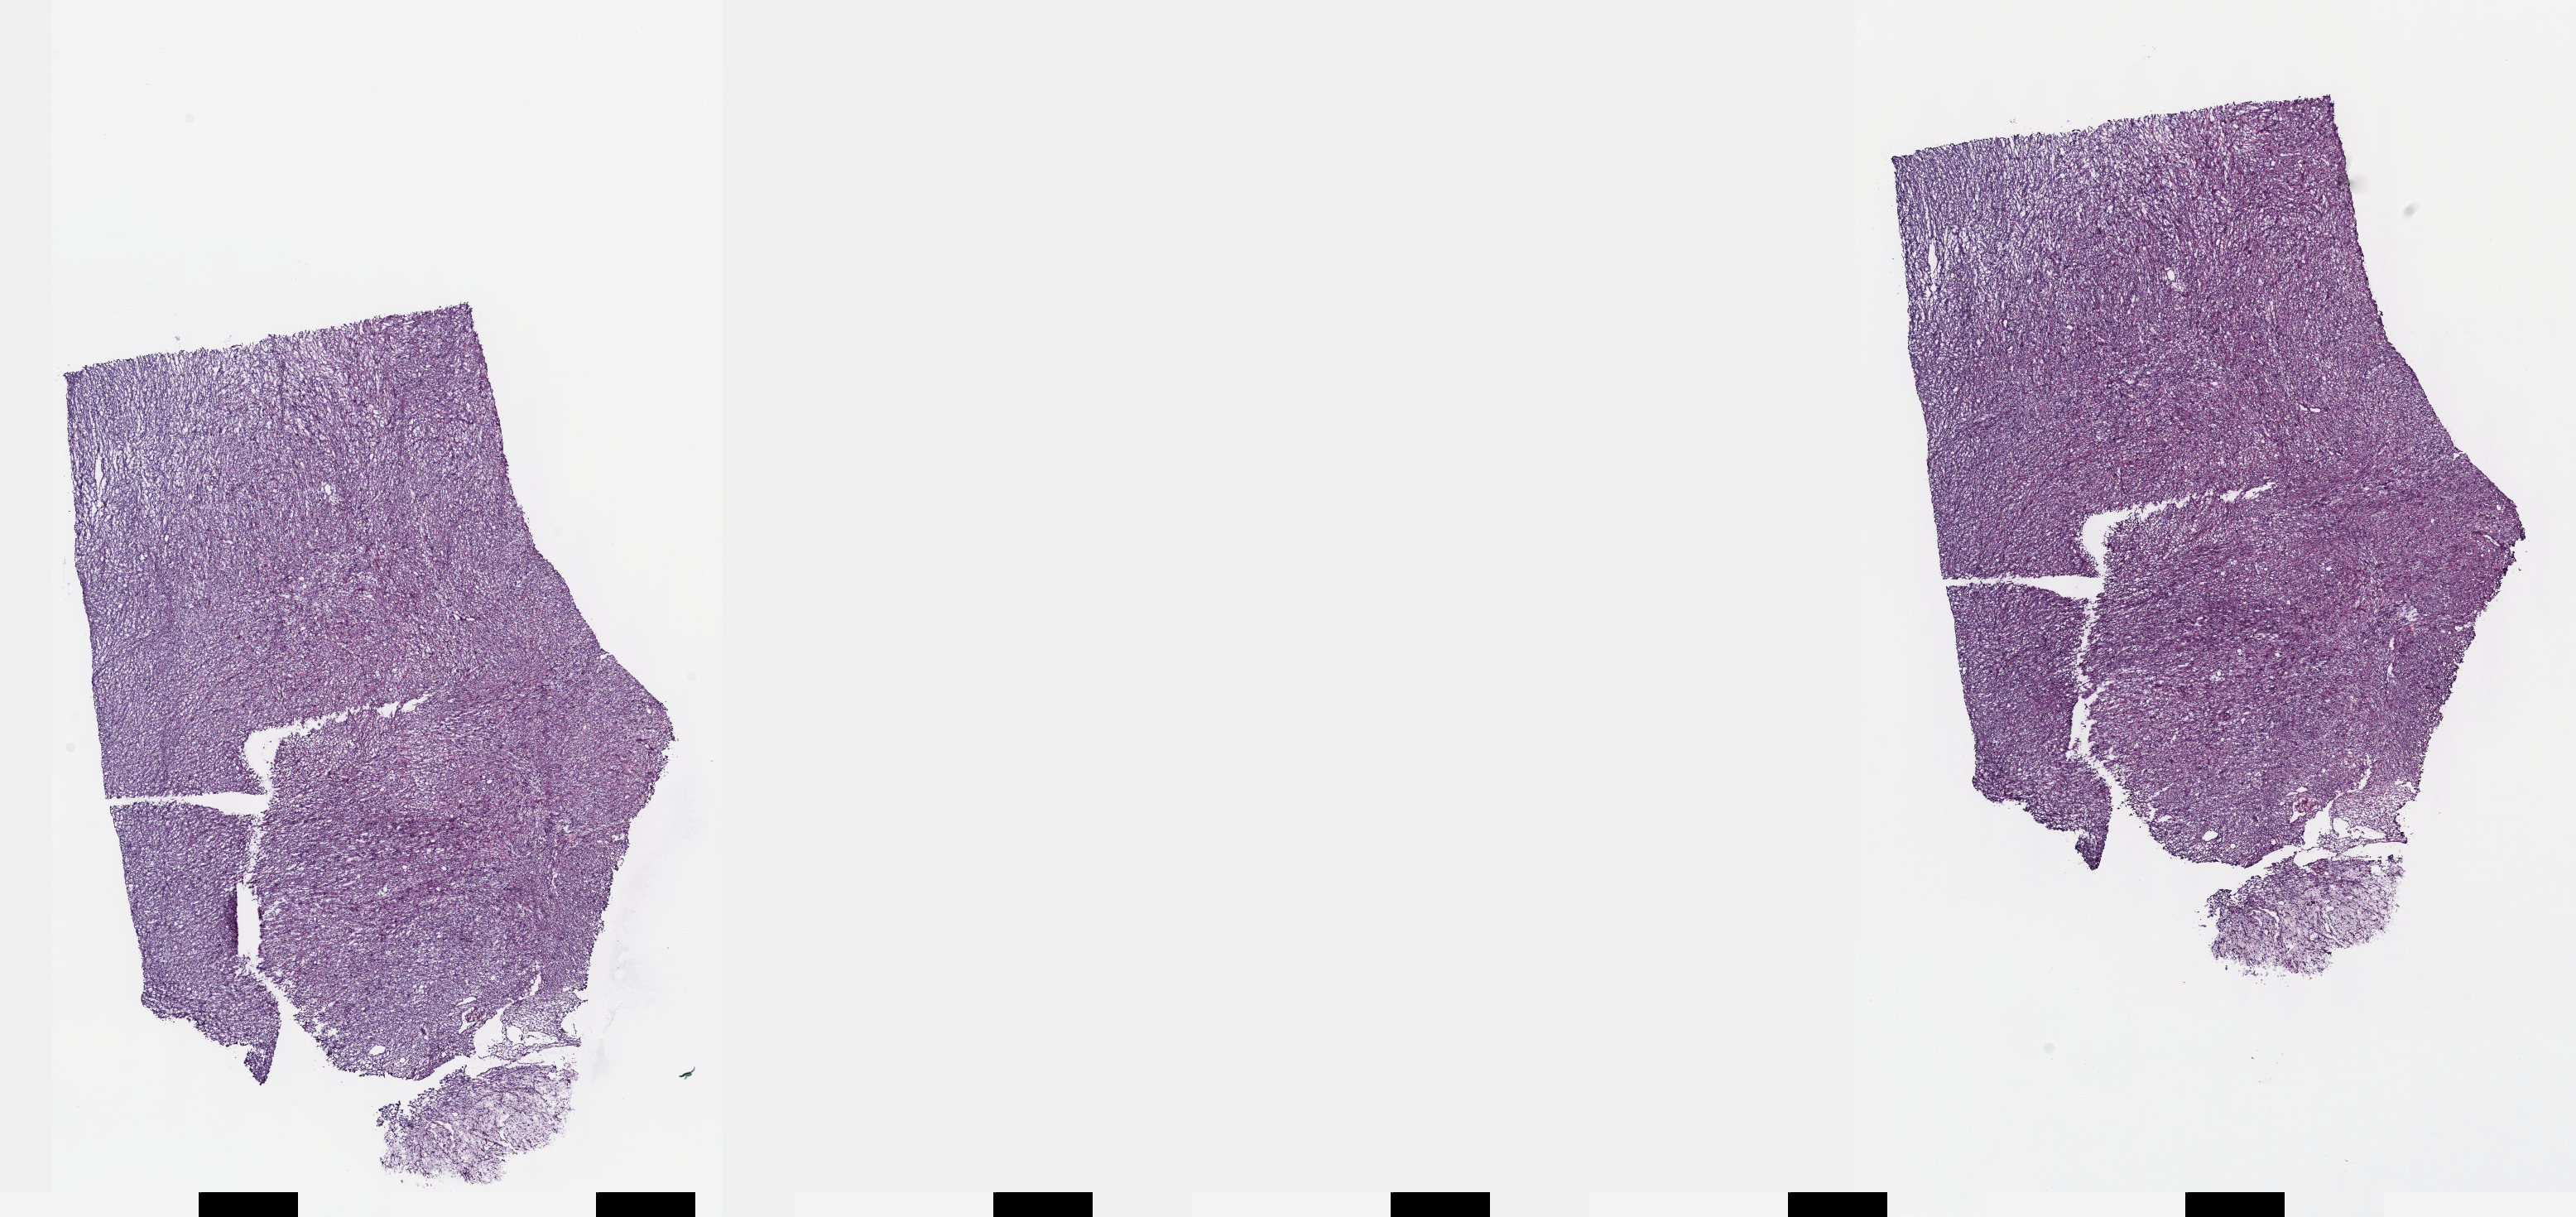
Digitized Hematoxylin and eosin (H&E) stained tissue section (whole slide), low-resolution overview of the scanned area, about 25.1 x 11.9 mm. Frozen section from the top of the tissue portion. Connective, subcutaneous and other soft tissues, primary tumour sample. Female, age 63 years at initial diagnosis. Pathologist review of this section (percent, as recorded): tumour cells 80%, tumour nuclei 80%, normal cells 0%, stromal cells 19%, necrosis 1%. Infiltration values recorded for this section: lymphocyte infiltration 2%, monocyte infiltration 1%, neutrophil infiltration 2%.
Diagnosis: Malignant fibrous histiocytoma (connective, subcutaneous and other soft tissues of thorax).